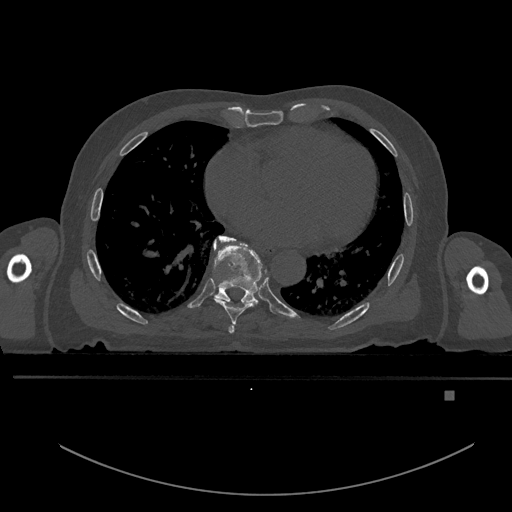
CT including the spine, one axial slice. Slice 229 of 969 in the series (ordered by position). Bone window (W 1800 / L 400 HU). 512 × 512 image matrix, field of view 456 × 456 mm. Patient: male, 82 years. From the clinical record (not read from this slice): primary cancer: prostate; vertebrae with lytic lesions (as recorded): T11, T9, T8, T2.
Structures marked on this image (semi-automatic segmentation, software-assisted and operator-edited):
- T6 vertebra: bounding box <228,325,234,333> (left, top, right, bottom; pixels)
- T7 vertebra: <216,235,267,324>
- T8 vertebra: <213,237,263,308>